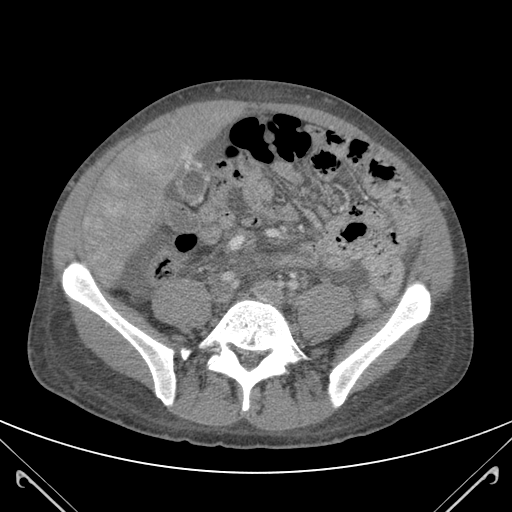
Contrast-enhanced abdominal CT (liver protocol), one axial slice; slice 25 of 118 in the series (ordered by position); soft-tissue window (W 400 / L 40 HU); 3 mm slice thickness; 512 × 512 image matrix. Case-level facts recorded for this patient, not image findings: diagnosis: hepatocellular carcinoma (patient treated with transarterial chemoembolisation; whether this scan precedes or follows treatment is not stated here); TNM stage (as recorded): Stage-IIIB; Child-Pugh class: A.
Outlined on this slice (semi-automatic segmentation, software-assisted and operator-edited):
- mass: bounding box (x1, y1, x2, y2) in pixels: (85, 151, 168, 261)